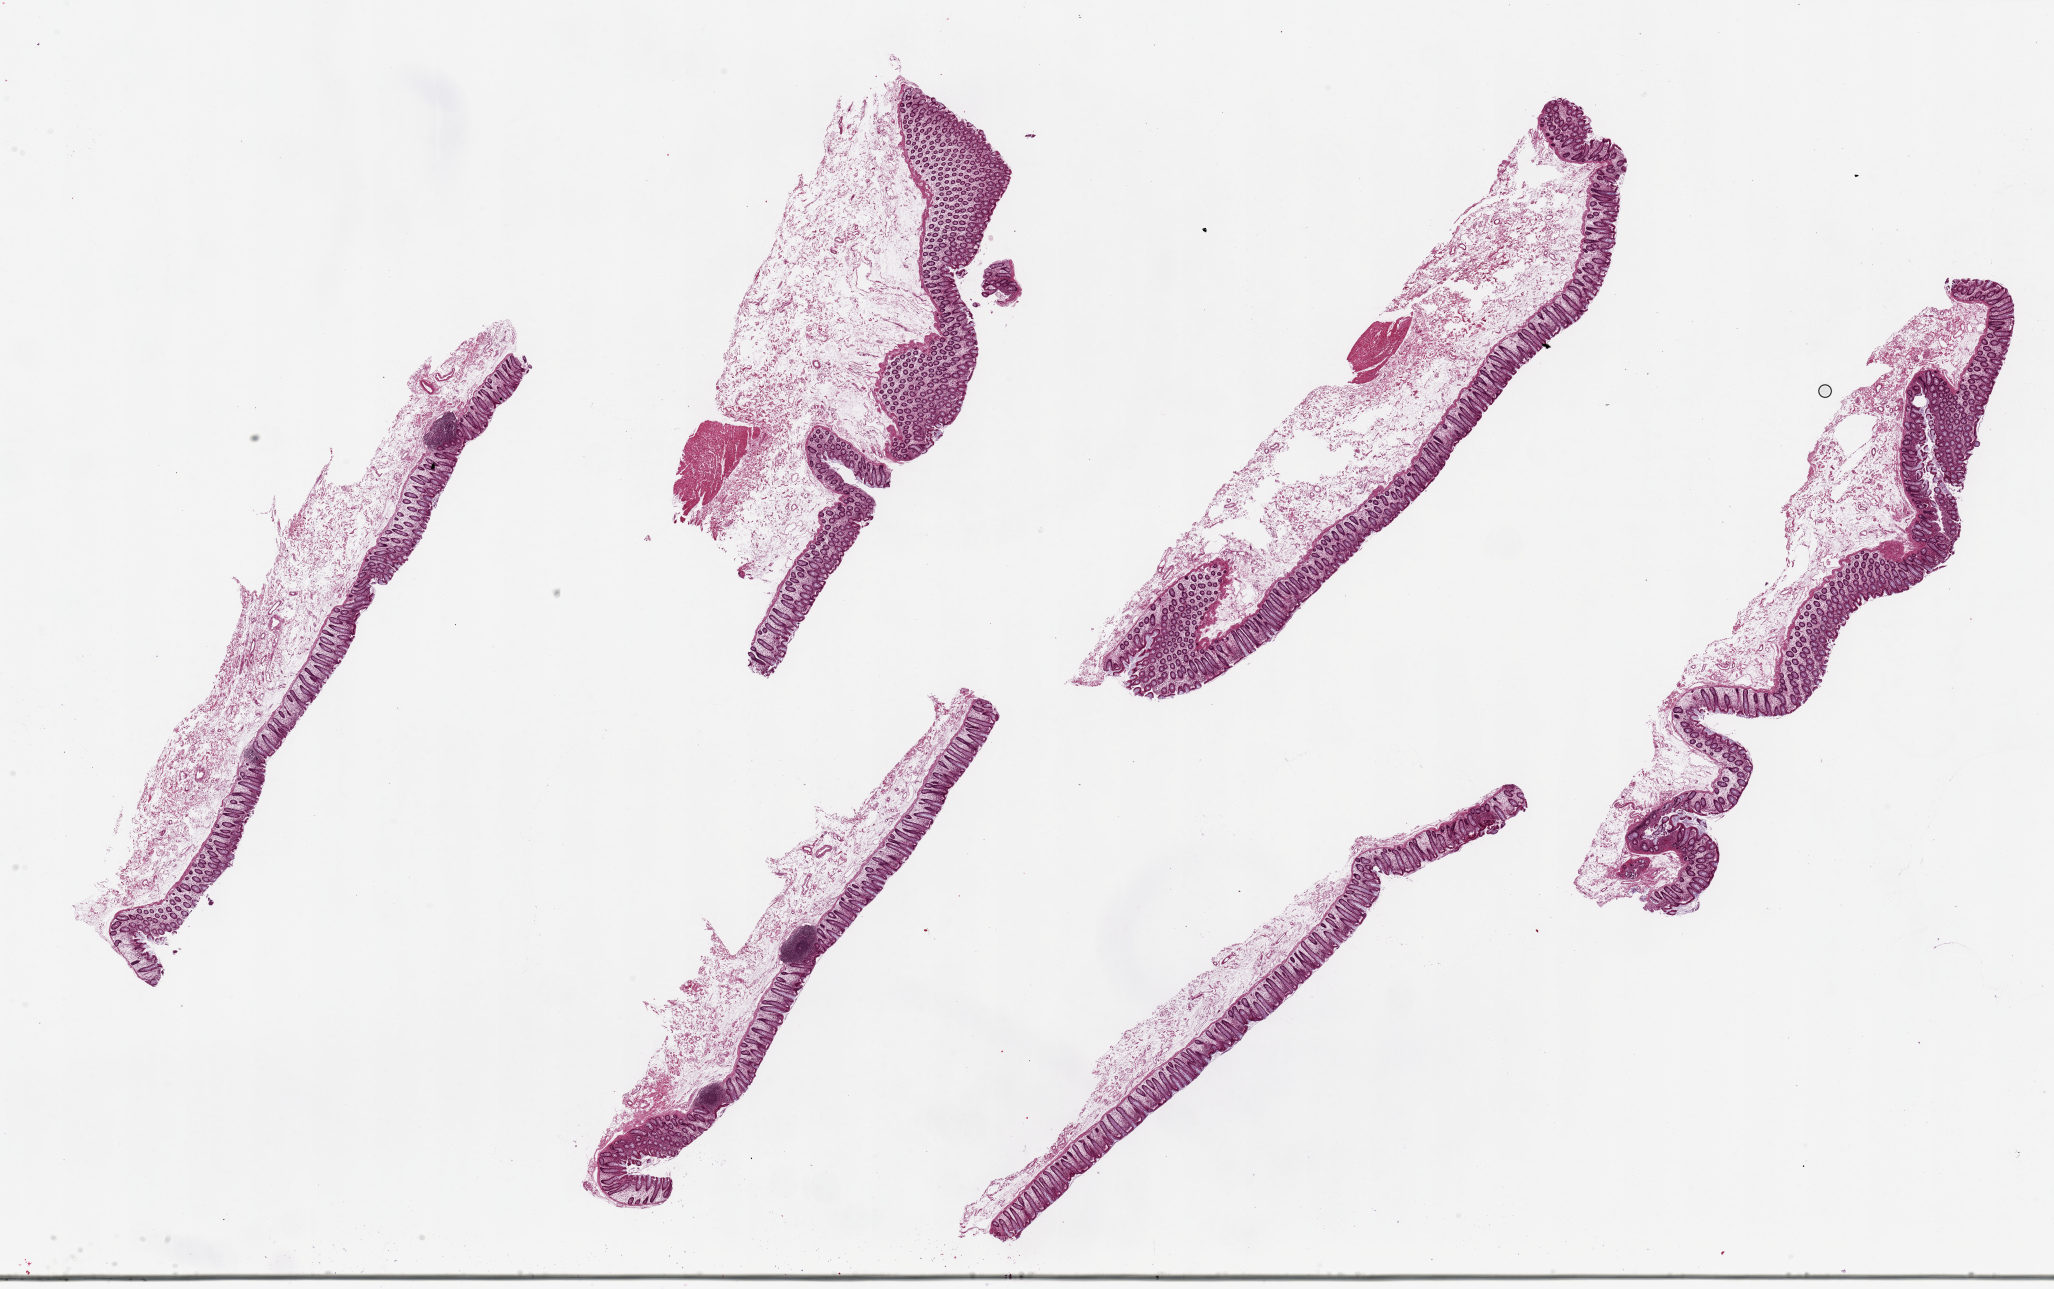
Whole-slide image, H&E stain, shown as a low-resolution overview of the whole scanned area (about 32.5 x 20.4 mm, slide scanned at 20x). PAXgene-fixed, paraffin-embedded tissue. Target tissue: transverse colon. Donor tissue sample. Donor: male.
- reviewer comment on this tissue sample: 6 pieces, up to 12x3 mm; good mucosa on all; hardly any muscularis